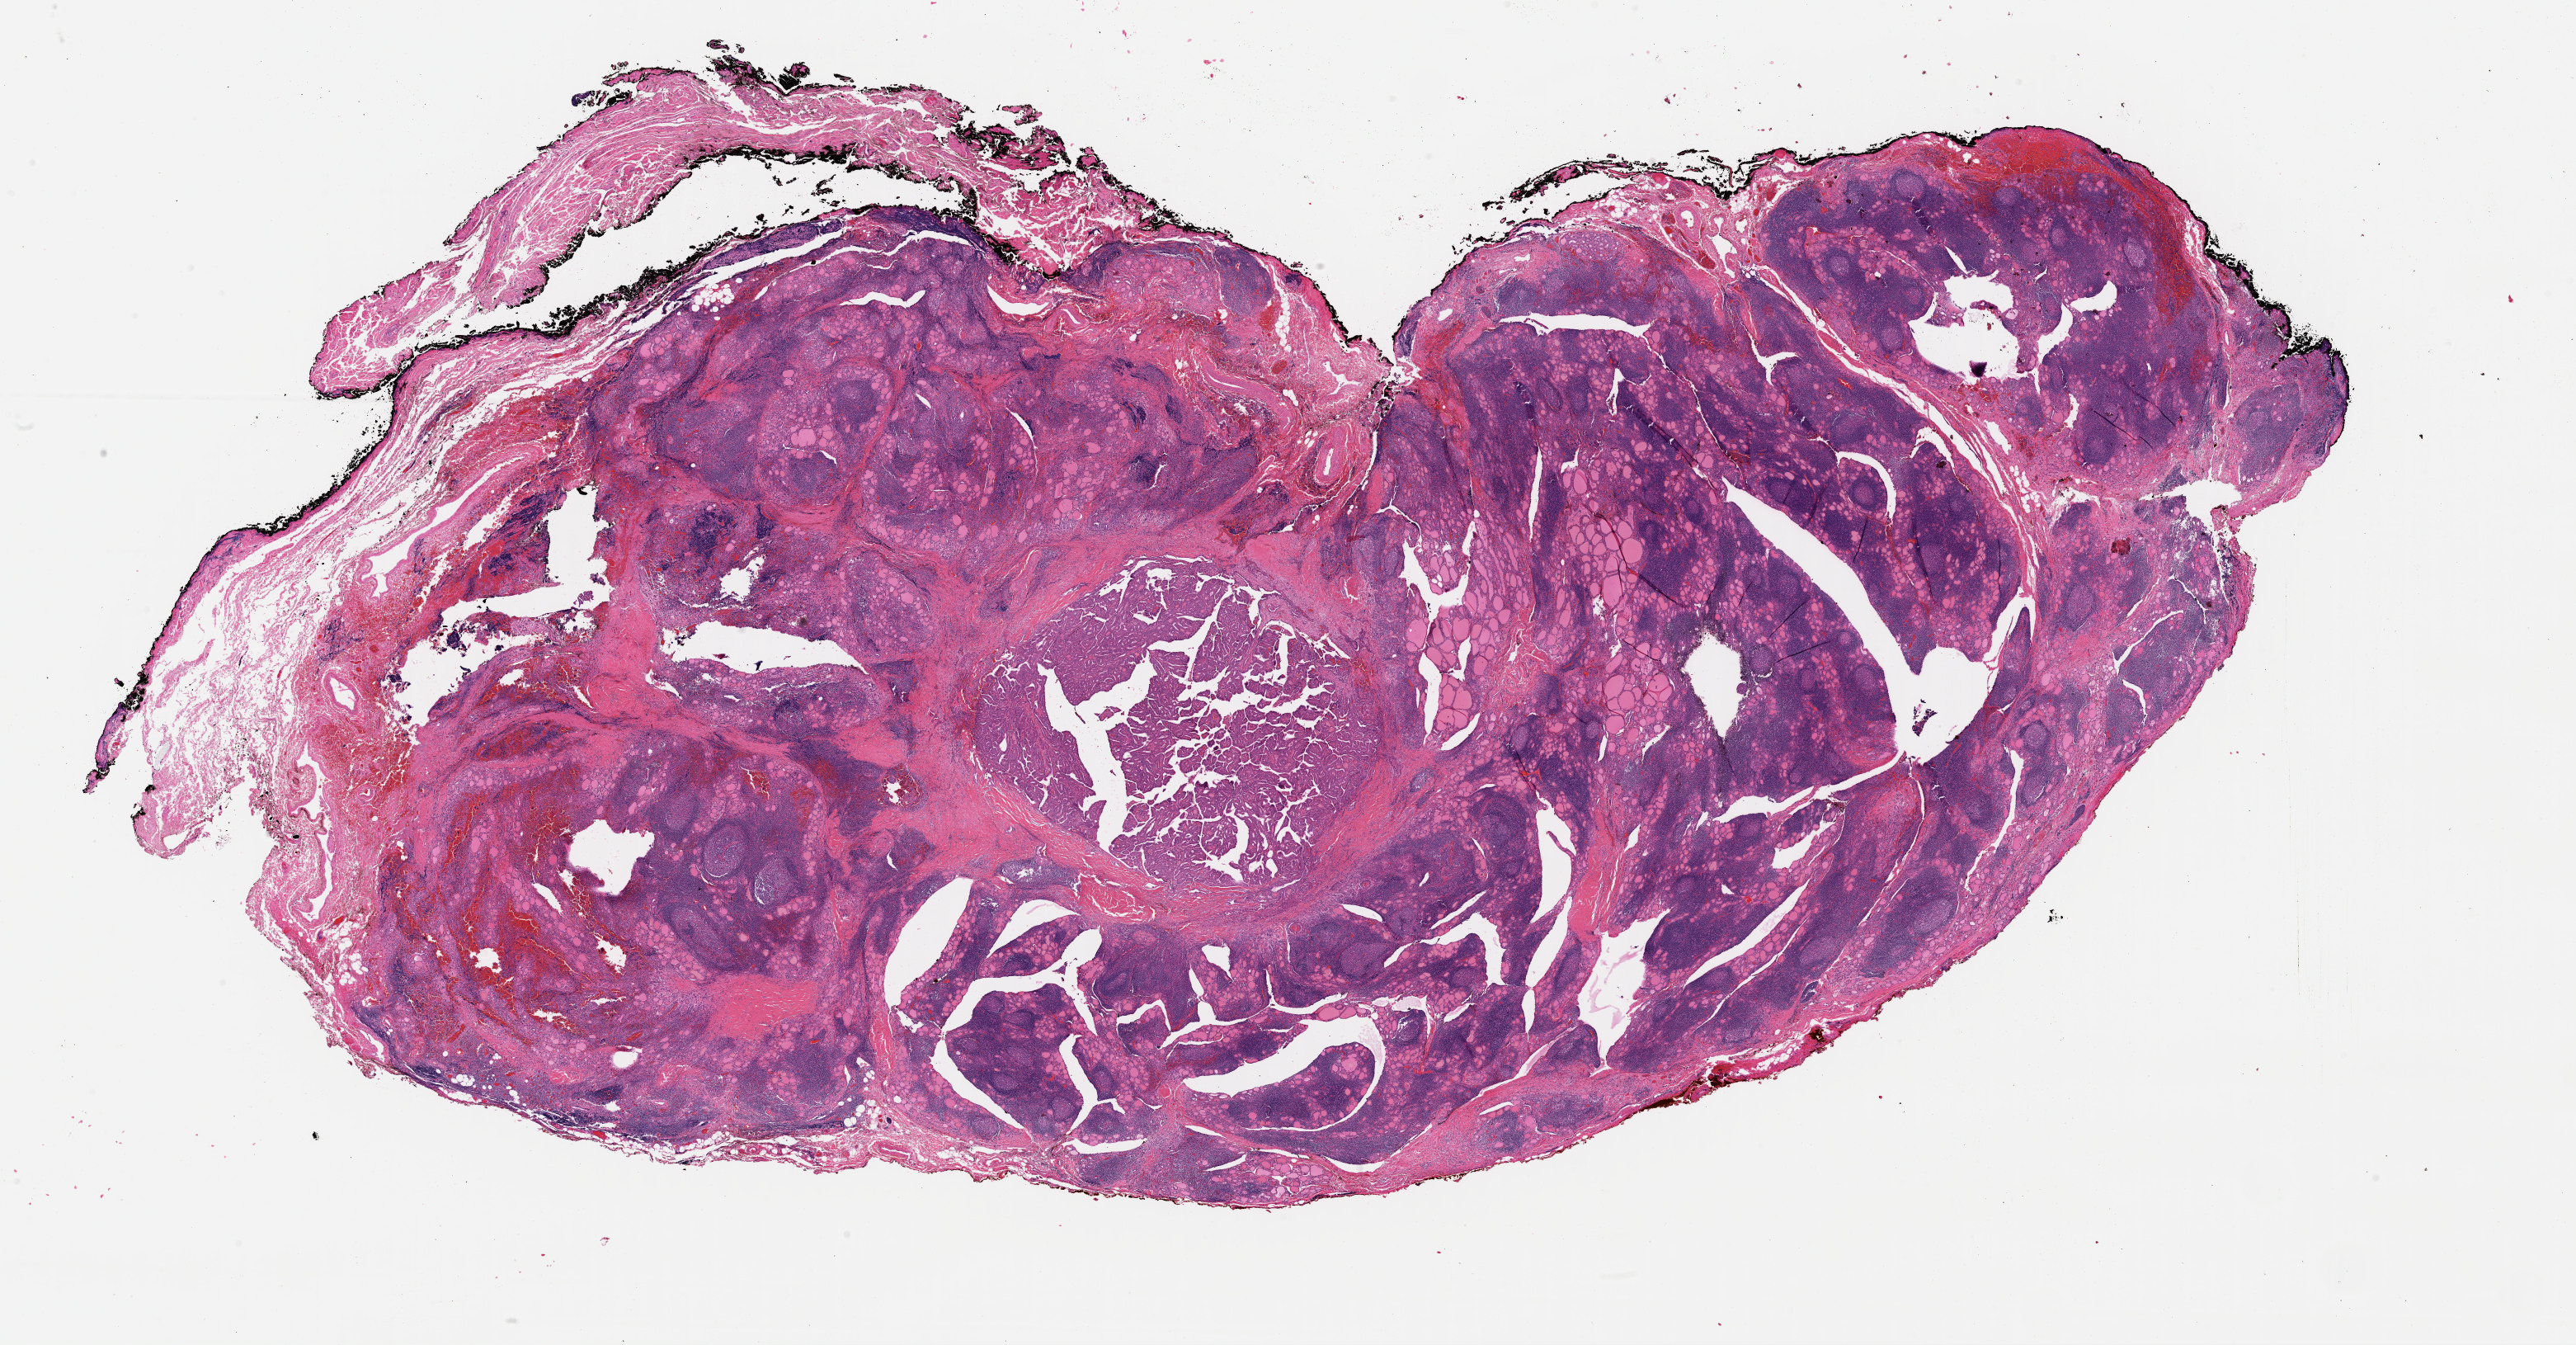
Whole-slide histology image, Hematoxylin and eosin (H&E) stained — low-resolution overview of the scanned area, about 24.7 x 12.9 mm, FFPE section, sample: primary tumour, thyroid. Female patient; age at initial diagnosis 33 years.
Pathologic diagnosis: Papillary adenocarcinoma, NOS (thyroid gland). AJCC pathologic stage: I (6th edition). Laterality: right.